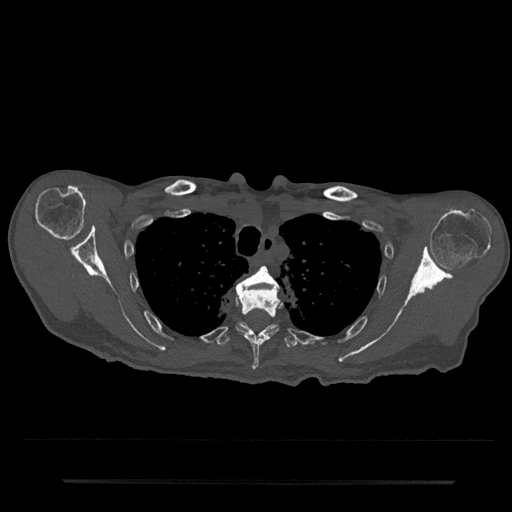
CT including the spine, one axial slice. Position 615 of 797 along the scan axis. Reconstruction kernel Br40s/3. 120 kVp. Bone window (W 1800 / L 400 HU). 512 × 512 image matrix, field of view 427 × 427 mm. Male patient, age 74 years. Case-level facts recorded for this patient, not image findings: primary cancer: prostate.
Annotated regions visible in this slice (semi-automatic segmentation, software-assisted and operator-edited):
- T3 vertebra: bounding box [x1, y1, x2, y2] px = [238, 266, 280, 290]
- T4 vertebra: [236, 286, 282, 370]
- T5 vertebra: [216, 322, 298, 348]